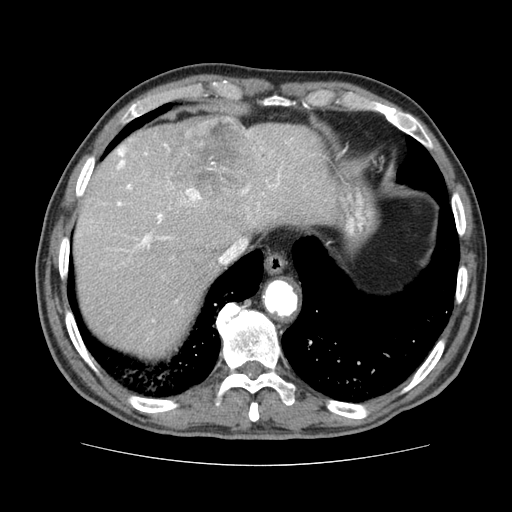
Contrast-enhanced abdominal CT (liver protocol), one axial slice; soft-tissue window (W 400 / L 40 HU); 2.5 mm slice thickness; 512 × 512 image matrix, field of view 360 × 360 mm. Case-level facts recorded for this patient, not image findings: diagnosis: hepatocellular carcinoma (patient treated with transarterial chemoembolisation; whether this scan precedes or follows treatment is not stated here); TNM stage (as recorded): Stage-I.
Outlined on this slice (semi-automatically segmented with operator editing):
- liver parenchyma outside the tumour (the mass and vessels are separate outlines, so this box may not span the whole liver): bounding box (x1, y1, x2, y2) in pixels: (74, 116, 339, 356)
- mass: (158, 115, 259, 208)
- liver vessels: (117, 146, 280, 247)